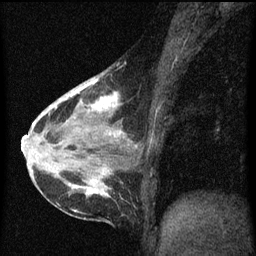
Breast MRI (dynamic contrast-enhanced), one sagittal slice. Slice 28 of 60 in the series (ordered by position). Dynamic contrast-enhanced series, image 2 of 3 at this slice position (ordered by acquisition). 1.5 T. TE 4.2 ms, TR 8 ms. 2 mm slice thickness. 256 × 256 image matrix. Patient: female, 38 years.
Structures marked on this image (semi-automatic segmentation, software-assisted and operator-edited):
- analysis volume of interest (the breast-tissue region the enhancement analysis was run in; not a lesion): box from (x=61, y=72) to (x=129, y=147) px
- tumour enhancement mask (voxels above the 70 % enhancement threshold inside the analysis volume of interest): (x=63, y=78)–(x=121, y=139)